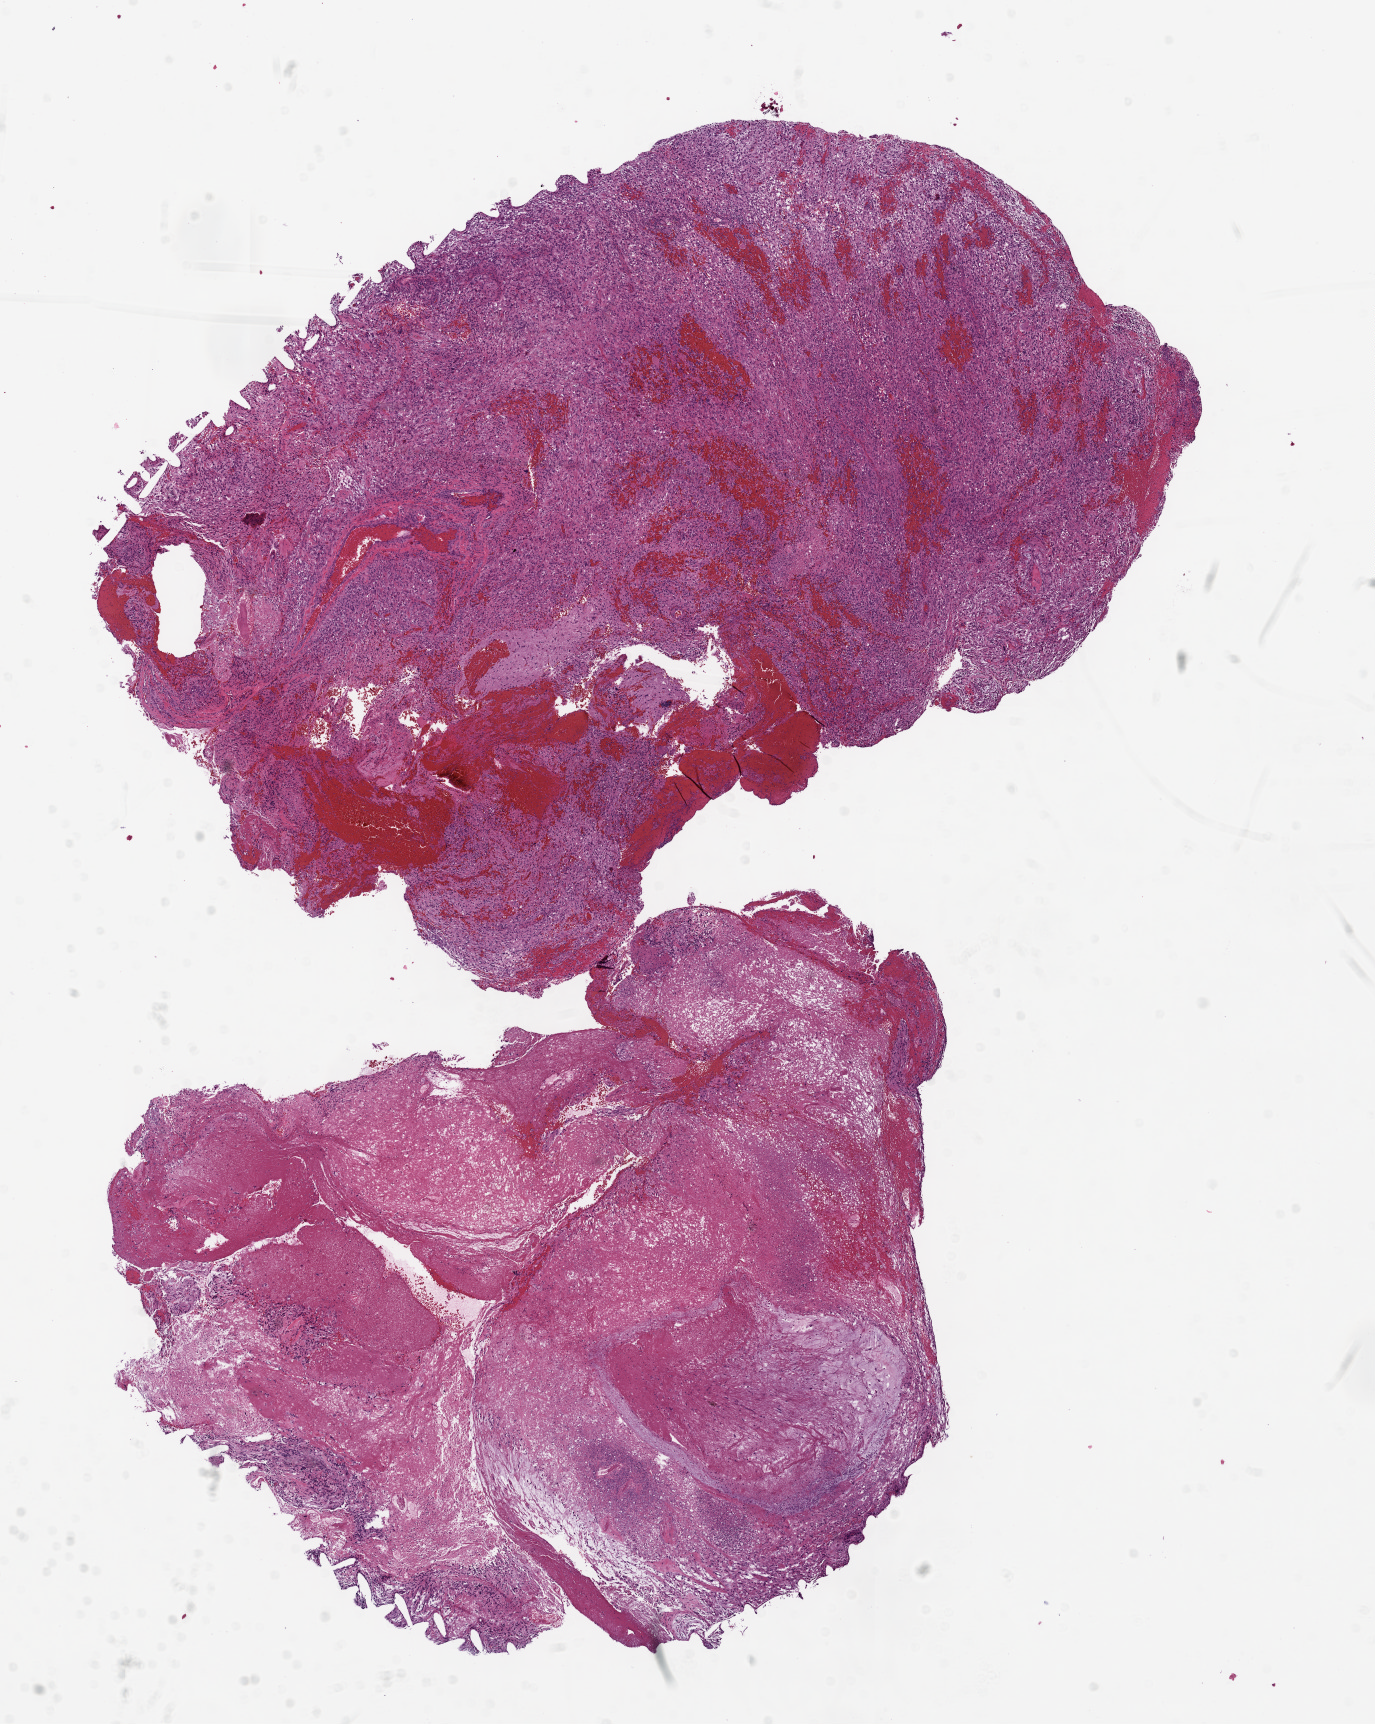
Whole-slide histology image, H&E — whole scanned area (about 11.0 x 13.8 mm) shown as a low-resolution overview, frozen section from the top of the tissue portion, brain, primary tumour sample. Male patient; age at initial diagnosis 48 years. Slide review estimates, as recorded: tumour cells 60%, tumour nuclei 80%, normal cells 0%, stromal cells 0%, necrosis 40%.
Histologic diagnosis: Glioblastoma.